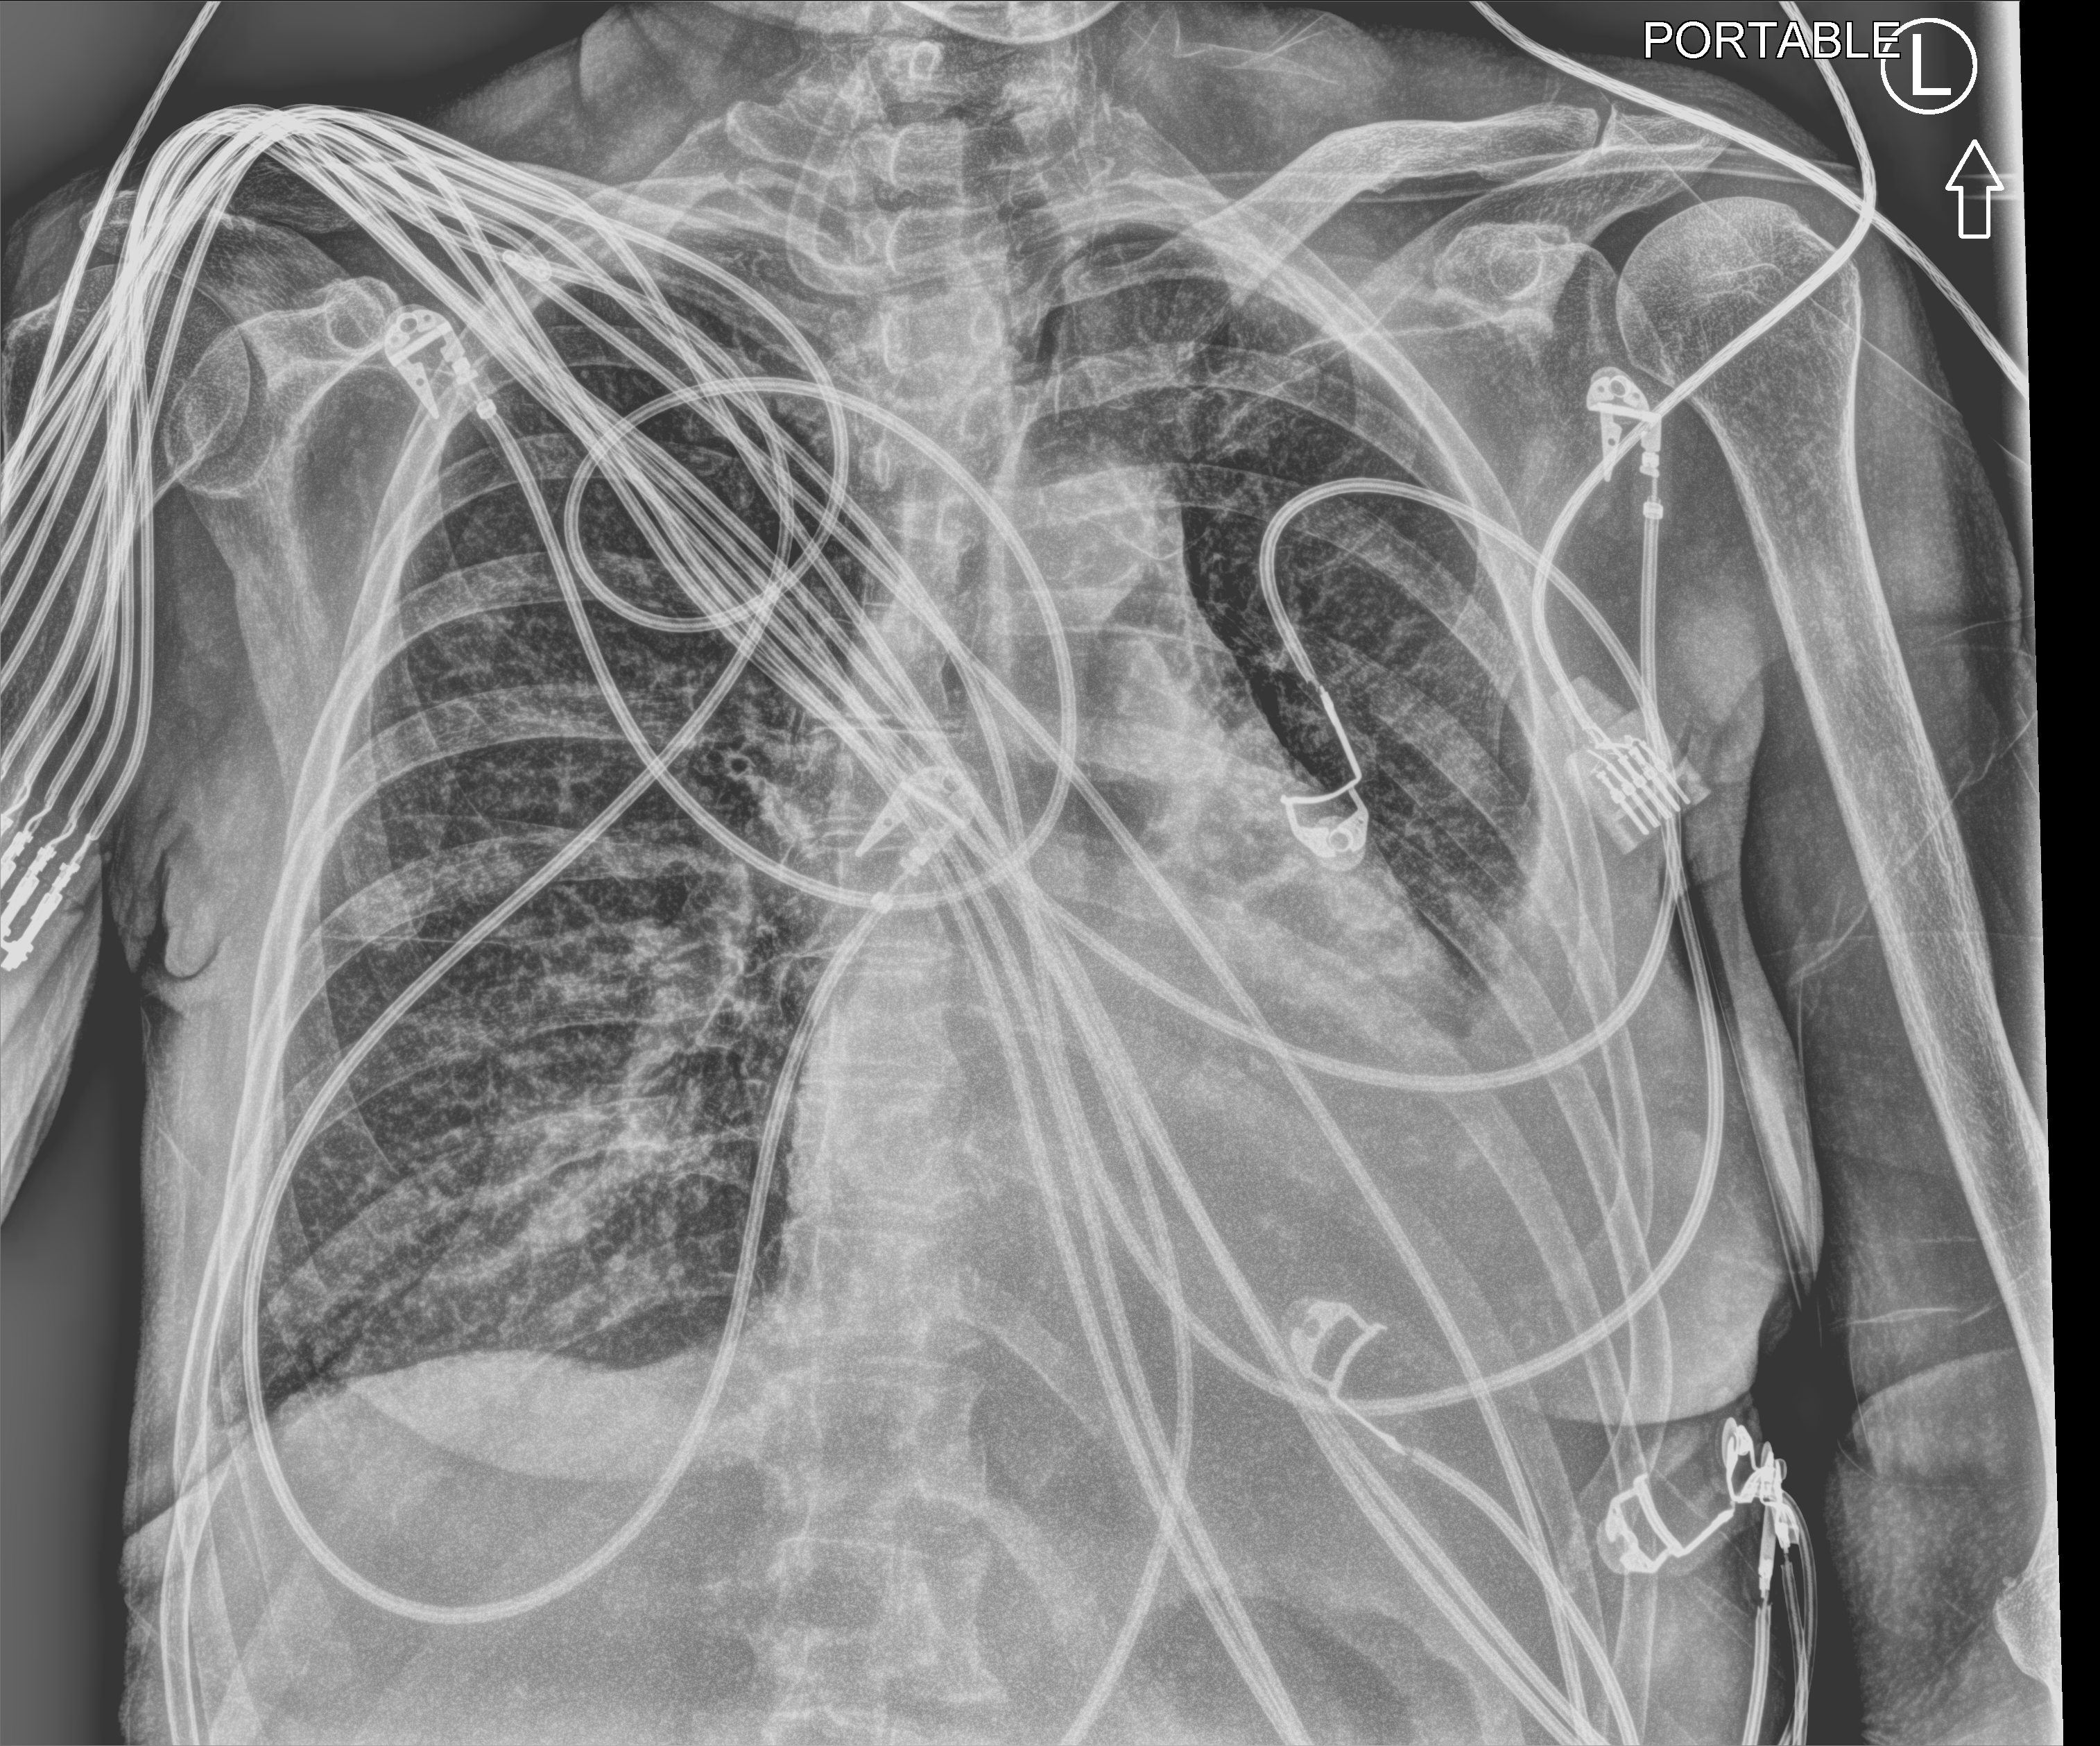
Portable chest radiograph; anteroposterior (AP) projection. Female patient hospitalised with COVID-19, age 60–74 years.
From the hospital-stay record, not from the radiograph (when in the stay this image was taken is not recorded): mechanically ventilated during this hospital stay: yes; admitted to intensive care during this hospital stay: yes.